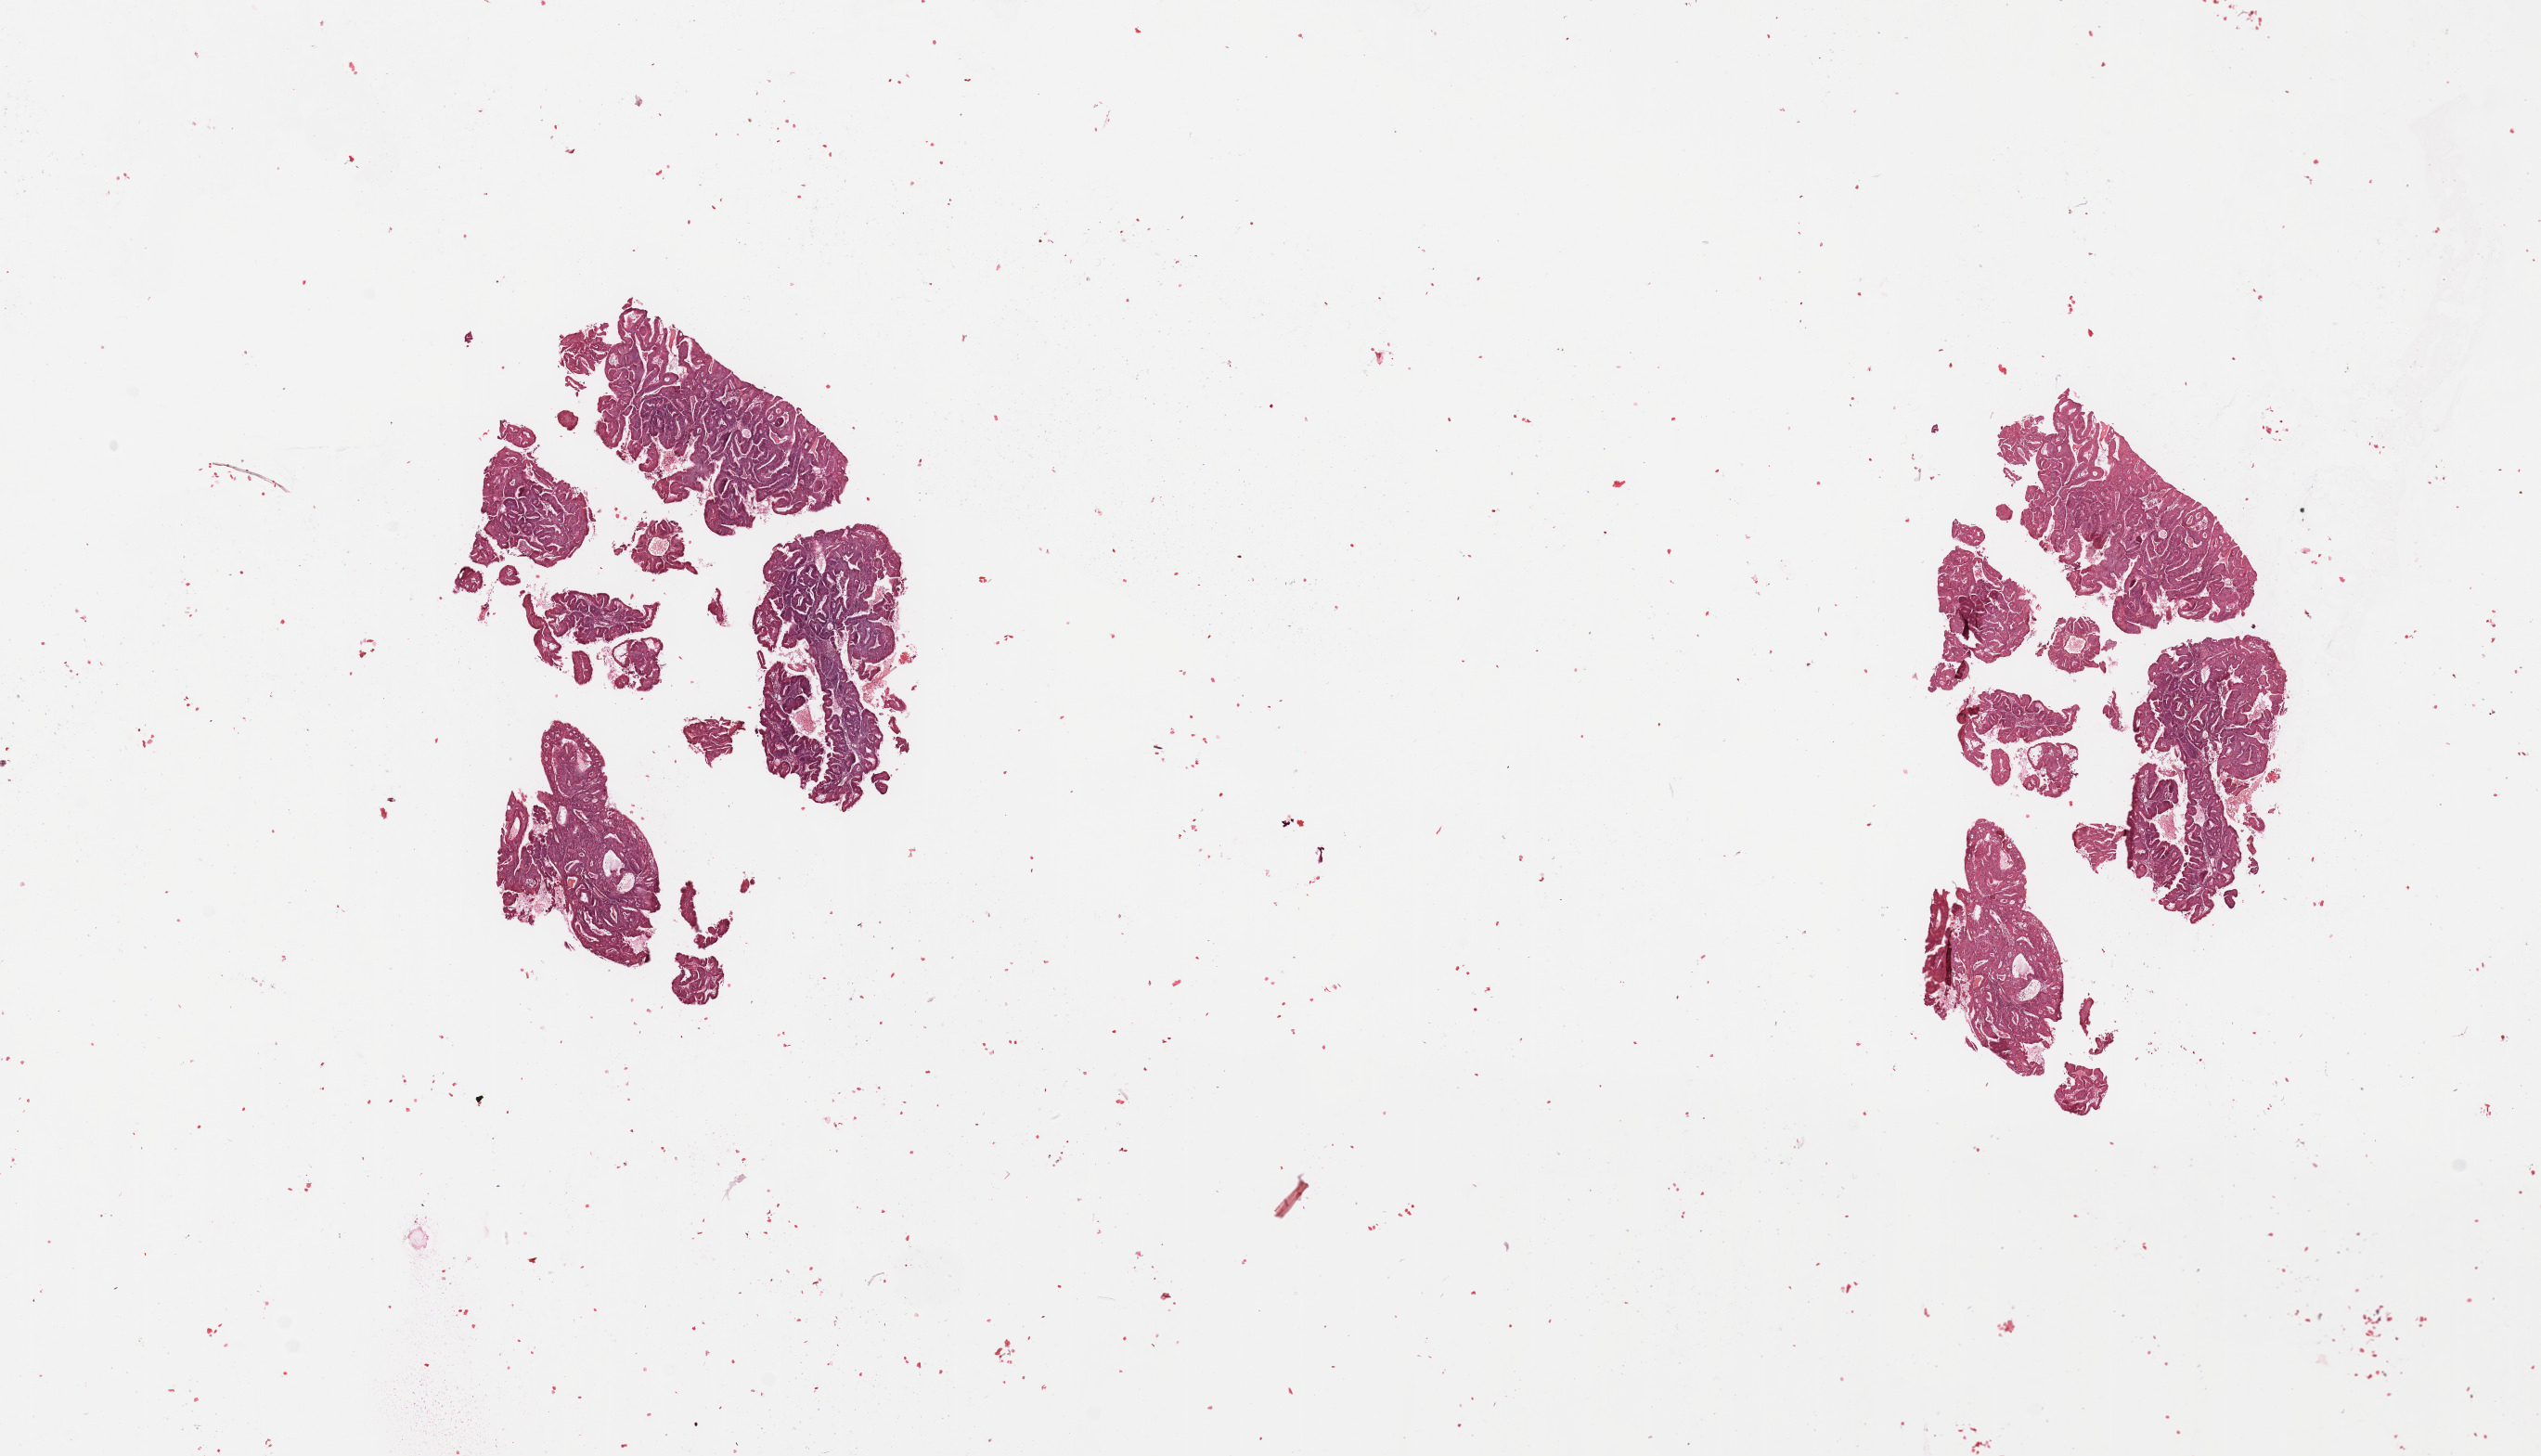
Whole-slide histology image, Hematoxylin and eosin (H&E) stained — whole scanned area (about 21.7 x 12.4 mm) shown as a low-resolution overview. Tumour tissue sample, sampled site: uterus. Female, 61 y/o. Histologic grade: G2 (moderately differentiated). Slide review estimates, as recorded: tumour nuclei 90%, necrosis 2%.
AJCC pathologic stage: I. Primary tumour site (as recorded): anterior endometrium. Histologic diagnosis: Endometrioid adenocarcinoma, NOS.